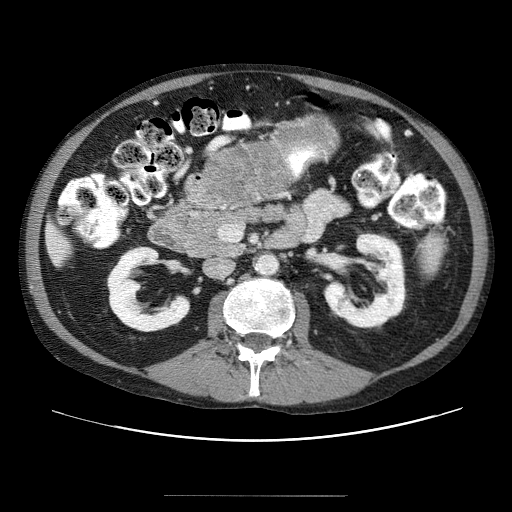
Contrast-enhanced abdominal CT (liver protocol), one axial slice. Slice 2 of 69 in the series (ordered by position). 120 kVp. Soft-tissue window (W 400 / L 40 HU). 2.5 mm slice thickness. 512 × 512 image matrix, field of view 380 × 380 mm. Case-level facts recorded for this patient, not image findings: diagnosis: hepatocellular carcinoma (patient treated with transarterial chemoembolisation; whether this scan precedes or follows treatment is not stated here); TNM stage (as recorded): Stage-IVB; Child-Pugh class: B.
Structures marked on this image (semi-automatic segmentation, software-assisted and operator-edited):
- liver parenchyma outside the tumour (the mass and vessels are separate outlines, so this box may not span the whole liver): box from (x=46, y=234) to (x=62, y=262) px
- mass: (x=209, y=150)–(x=280, y=201)